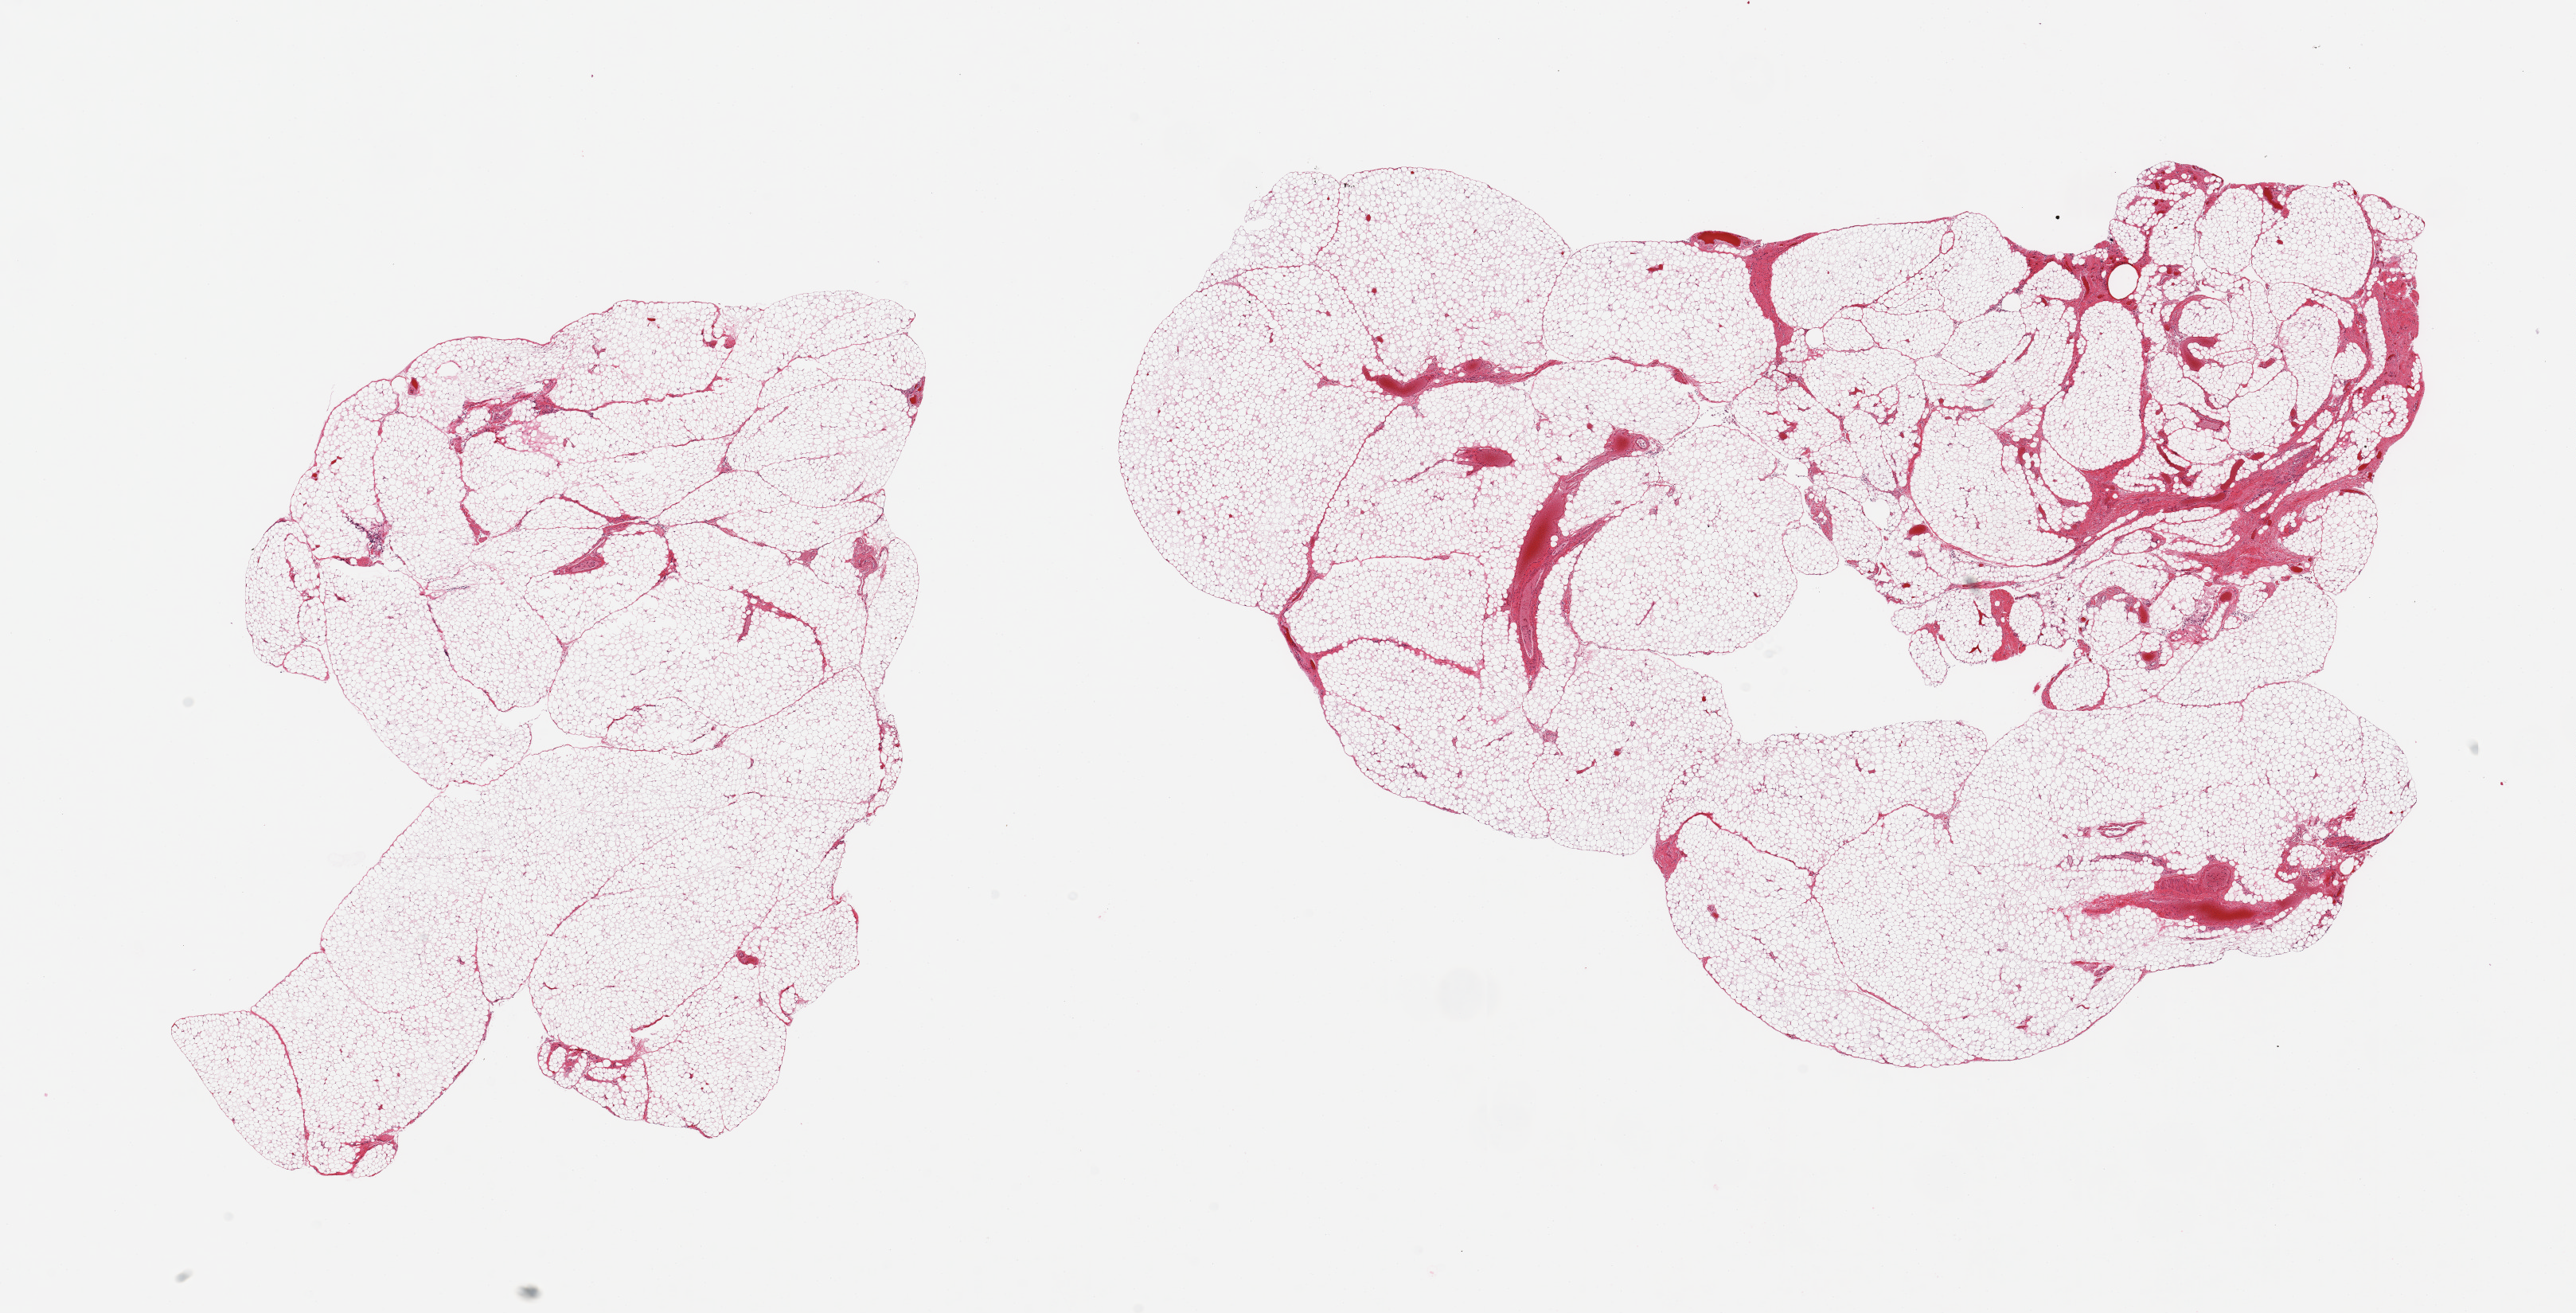
H&E whole-slide image, brightfield — whole scanned area (about 25.6 x 13.0 mm) shown as a low-resolution overview. PAXgene-fixed paraffin-embedded (PFPE) section. Sampled site (target tissue): omentum. Donor tissue sample. Donor sex: female.
Pathologist's review note for this sample: 2 pieces; lobulated mature adipose tissue with small fibrovascular component.